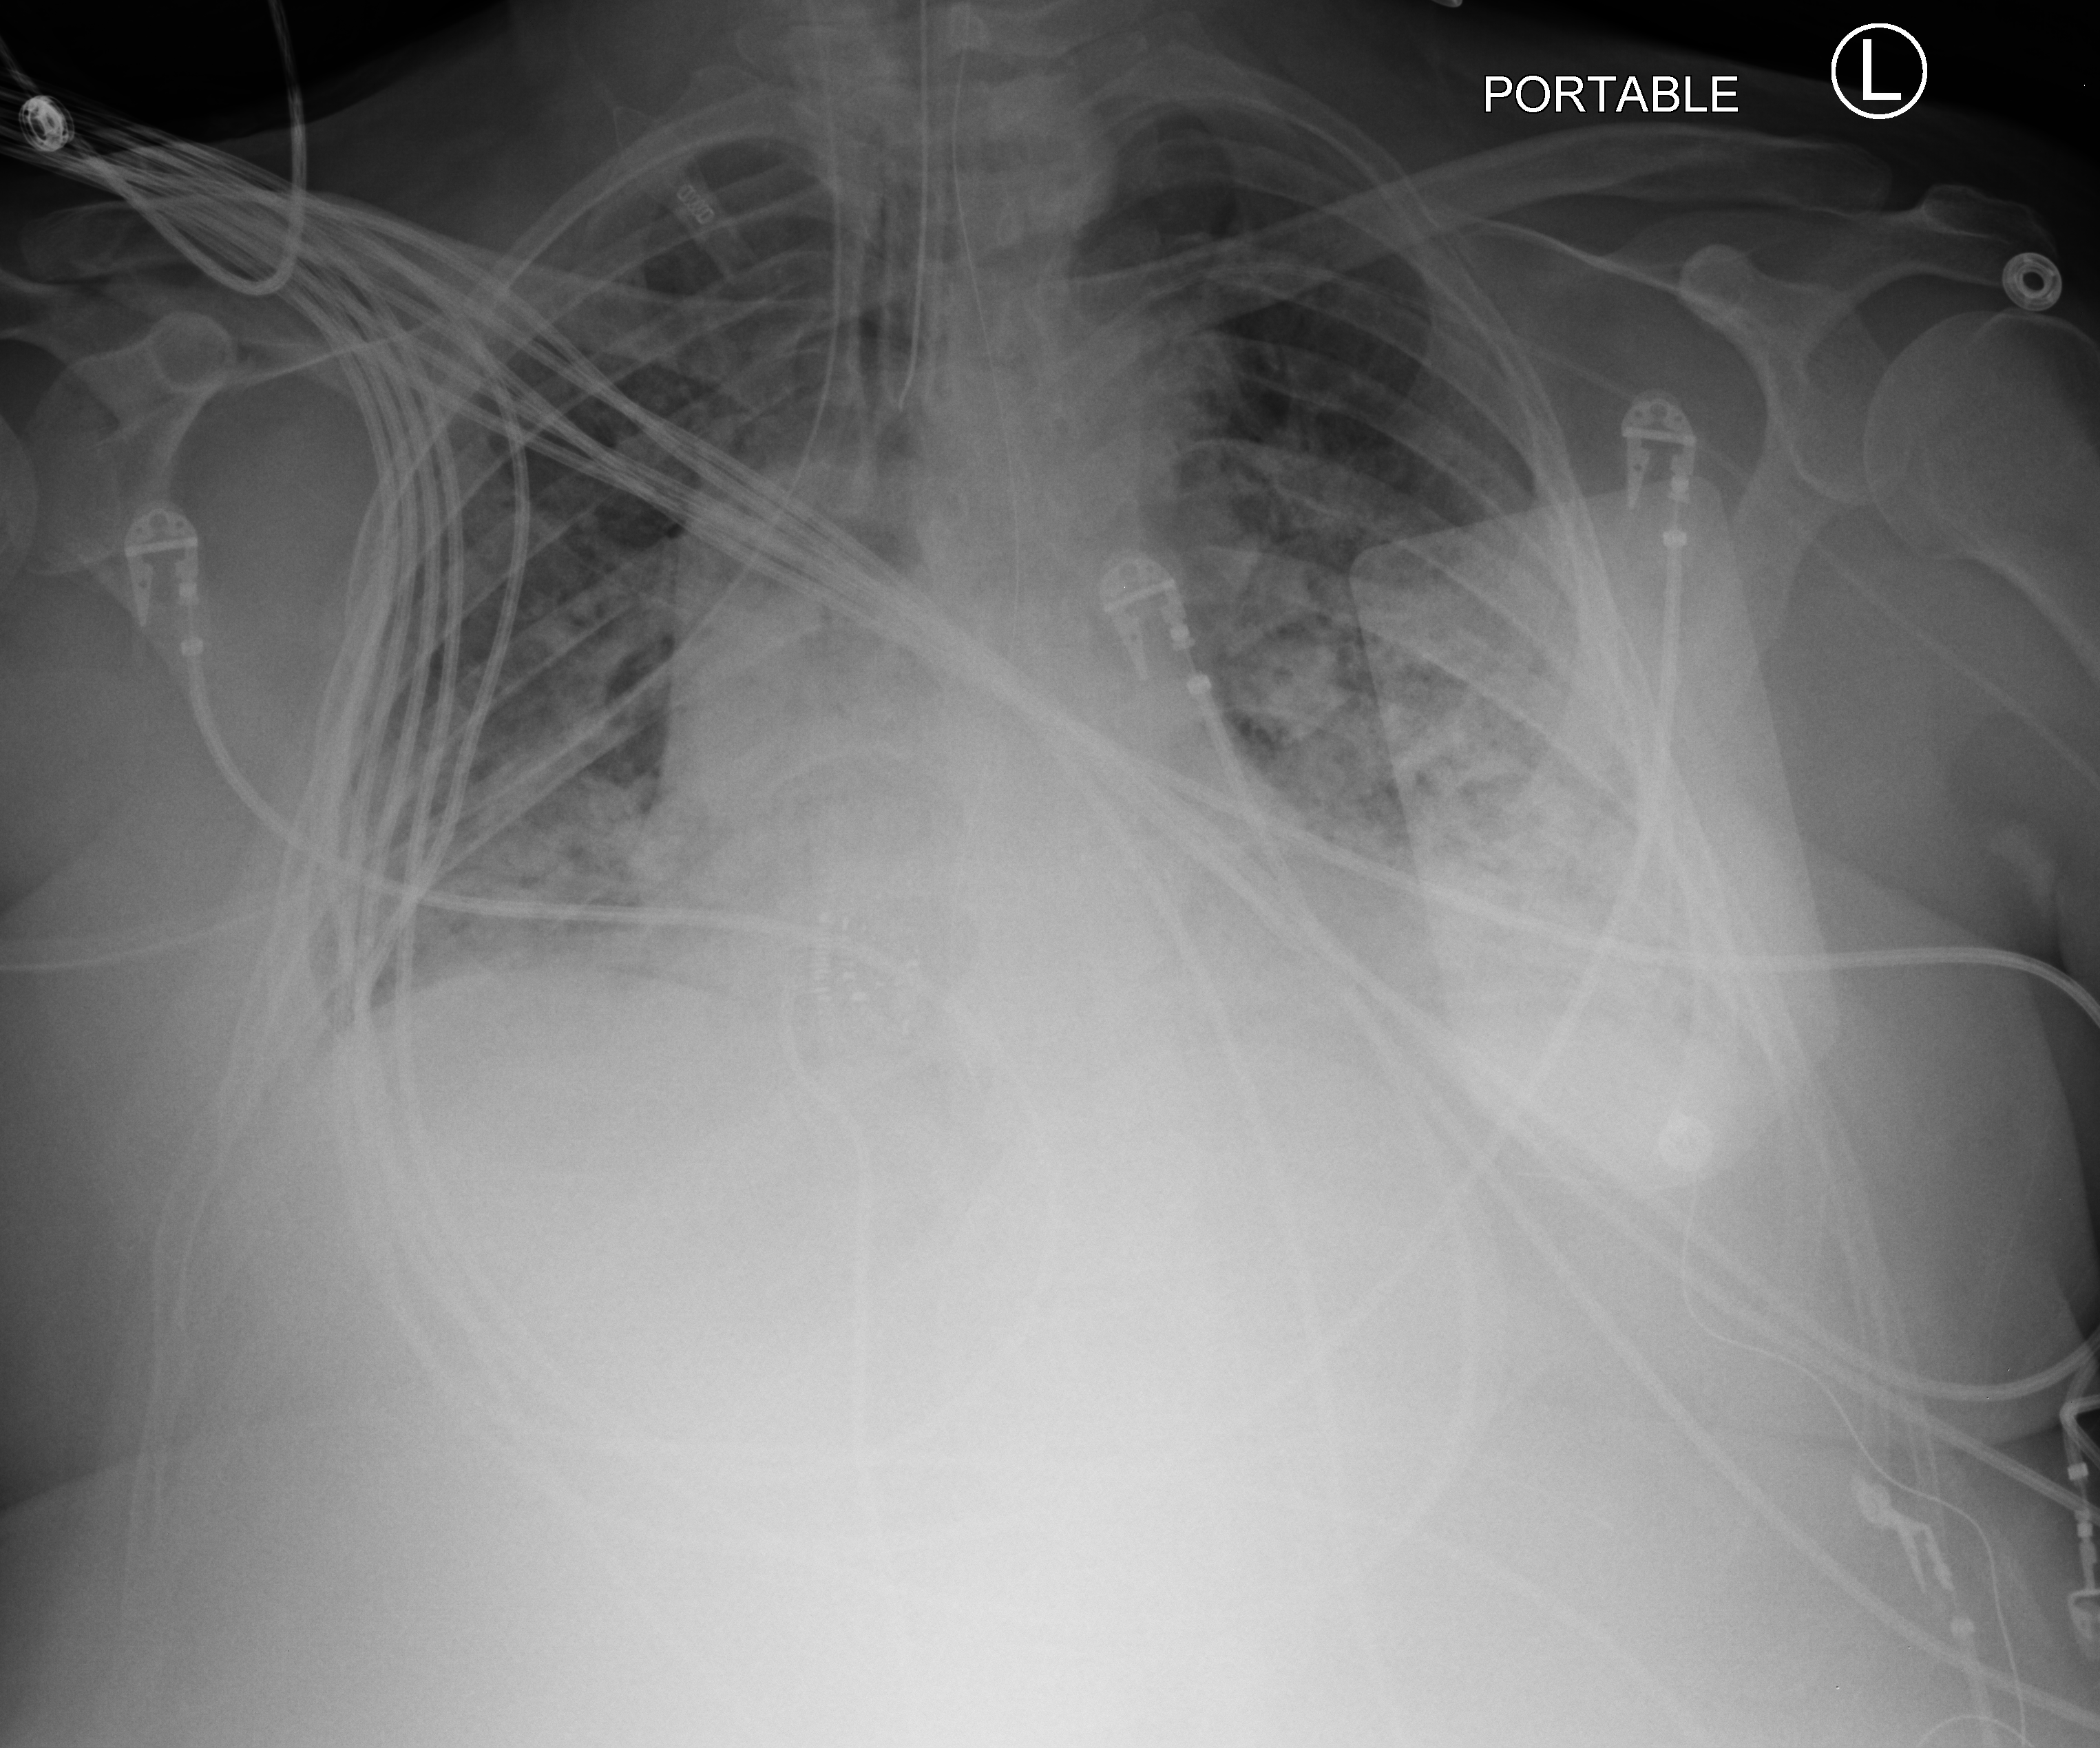
Portable chest radiograph, anteroposterior (AP) projection. Patient hospitalised with COVID-19; male, aged 18–59 years.
Hospital-stay facts (about this admission, not read from this image; timing relative to this image not recorded):
- mechanically ventilated during this hospital stay: yes
- admitted to intensive care during this hospital stay: yes